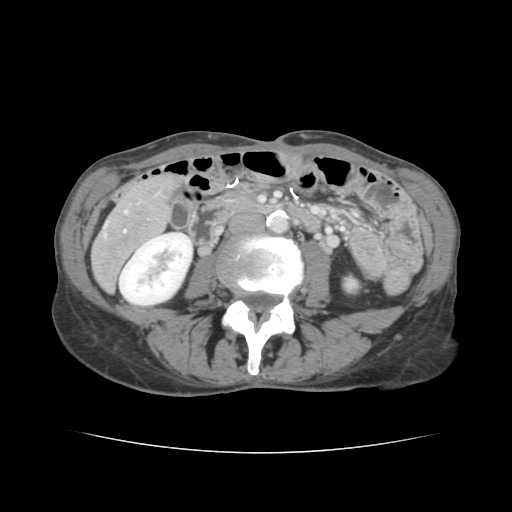
Contrast-enhanced abdominal CT, one axial slice. Slice 34 of 136 in the series (ordered by position). 120 kVp. Intravenous contrast given. Soft-tissue window (W 400 / L 40 HU). 512 × 512 image matrix. Female patient, age 77 years. Case-level facts recorded for this patient, not image findings: diagnosis: colorectal cancer liver metastases, imaged before liver resection; multiple liver metastases: yes; largest metastasis: 3 cm.
Outlined on this slice (manually delineated by an expert):
- liver: bounding box <93,176,176,288> (left, top, right, bottom; pixels)
- portal vein (with intrahepatic branches): <124,230,126,232>